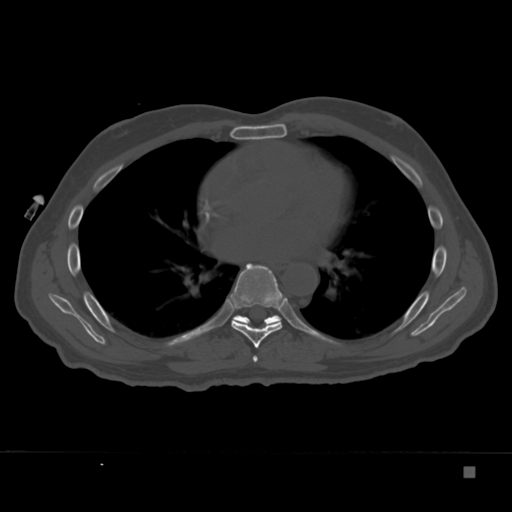
CT including the spine, one axial slice. Position 219 of 332 along the scan axis. 120 kVp. Bone window (W 1800 / L 400 HU). 1.5 mm slice thickness. 512 × 512 image matrix, field of view 389 × 389 mm. Male patient, age 72 years. From the clinical record (not read from this slice): primary cancer: skeletal.
Outlined on this slice (semi-automatic segmentation, software-assisted and operator-edited):
- T6 vertebra: bounding box [x1, y1, x2, y2] px = [253, 355, 258, 362]
- T7 vertebra: [229, 263, 285, 348]
- T8 vertebra: [233, 315, 281, 326]